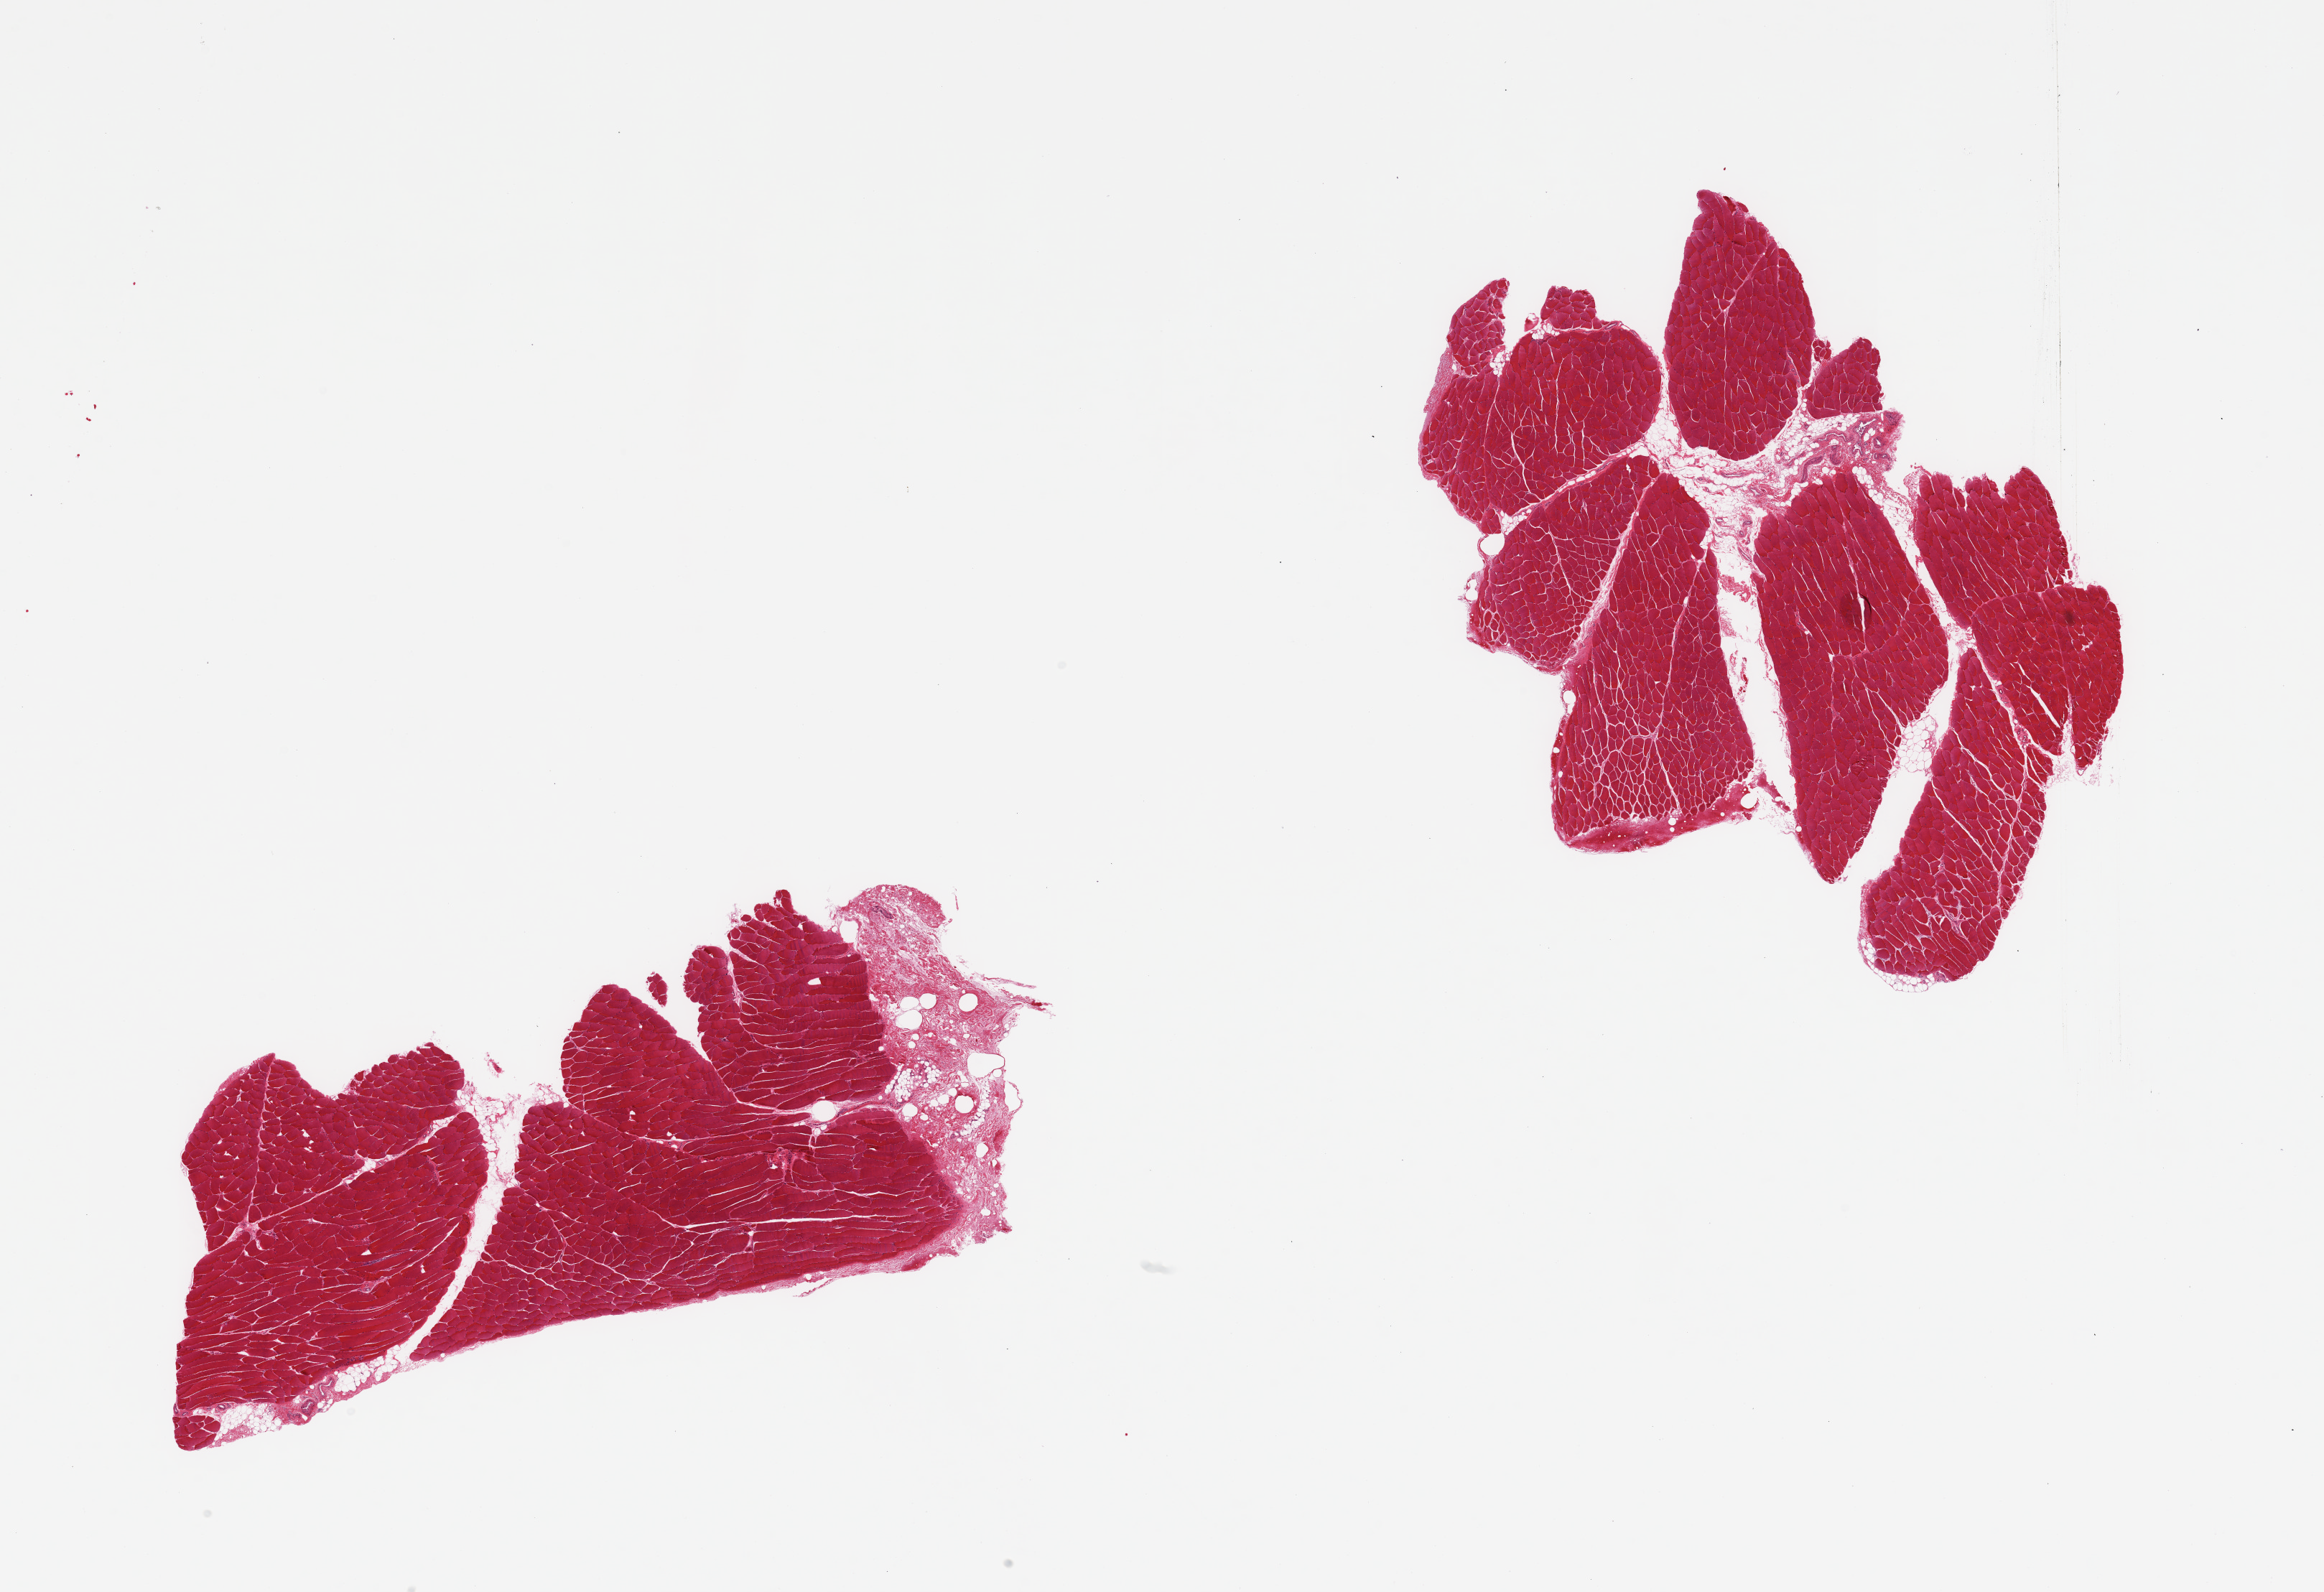
Haematoxylin and eosin whole-slide image — low-resolution overview of the scanned area, about 25.6 x 17.5 mm (acquisition: 20x scan); PAXgene-fixed, paraffin-embedded tissue; target tissue: skeletal muscle; donor tissue sample. Donor sex: male.
Pathologist's review note for this sample: 2 pieces, ~10% interstitial/adherent fat/vascular elements.